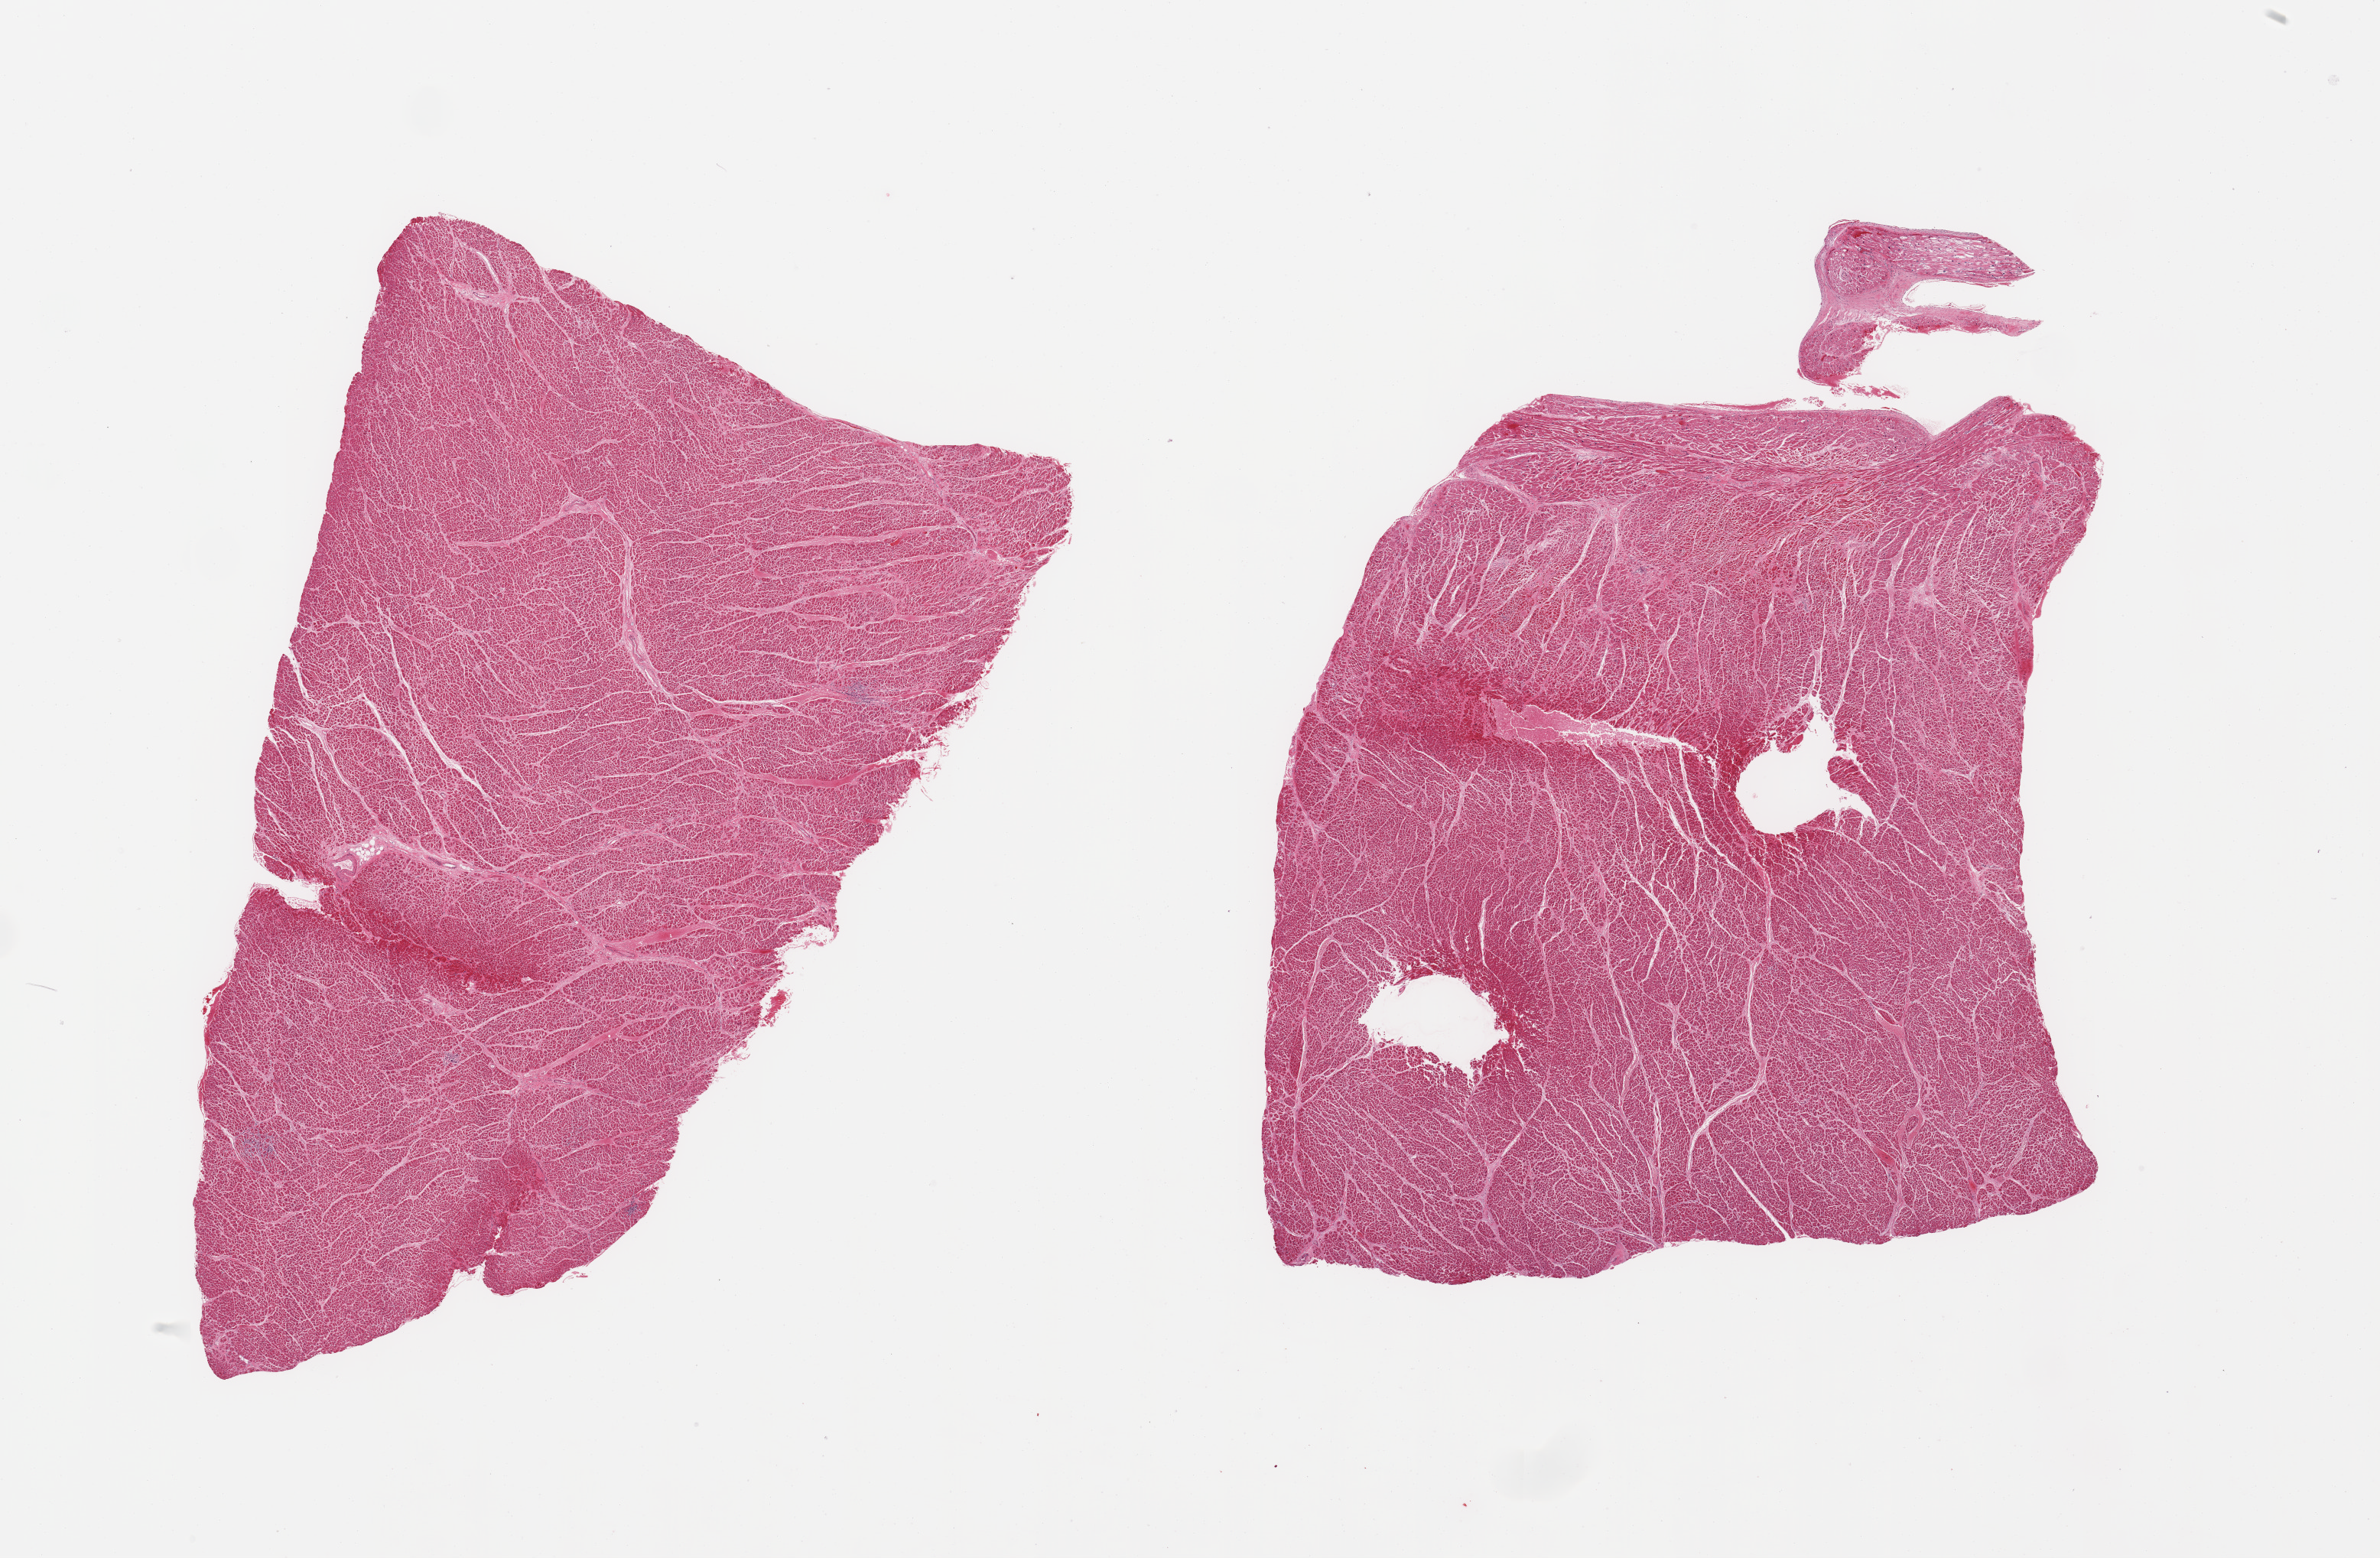
Digitized hematoxylin and eosin (H&E)-stained section — whole scanned area (about 24.6 x 16.1 mm, slide scanned at 20x) shown as a low-resolution overview, PAXgene-fixed paraffin-embedded (PFPE) section, sampled site (target tissue): heart, tissue donor sample. Male donor.
Review note (as recorded): 2 pieces; several small foci of myofiber damage or drop-out.